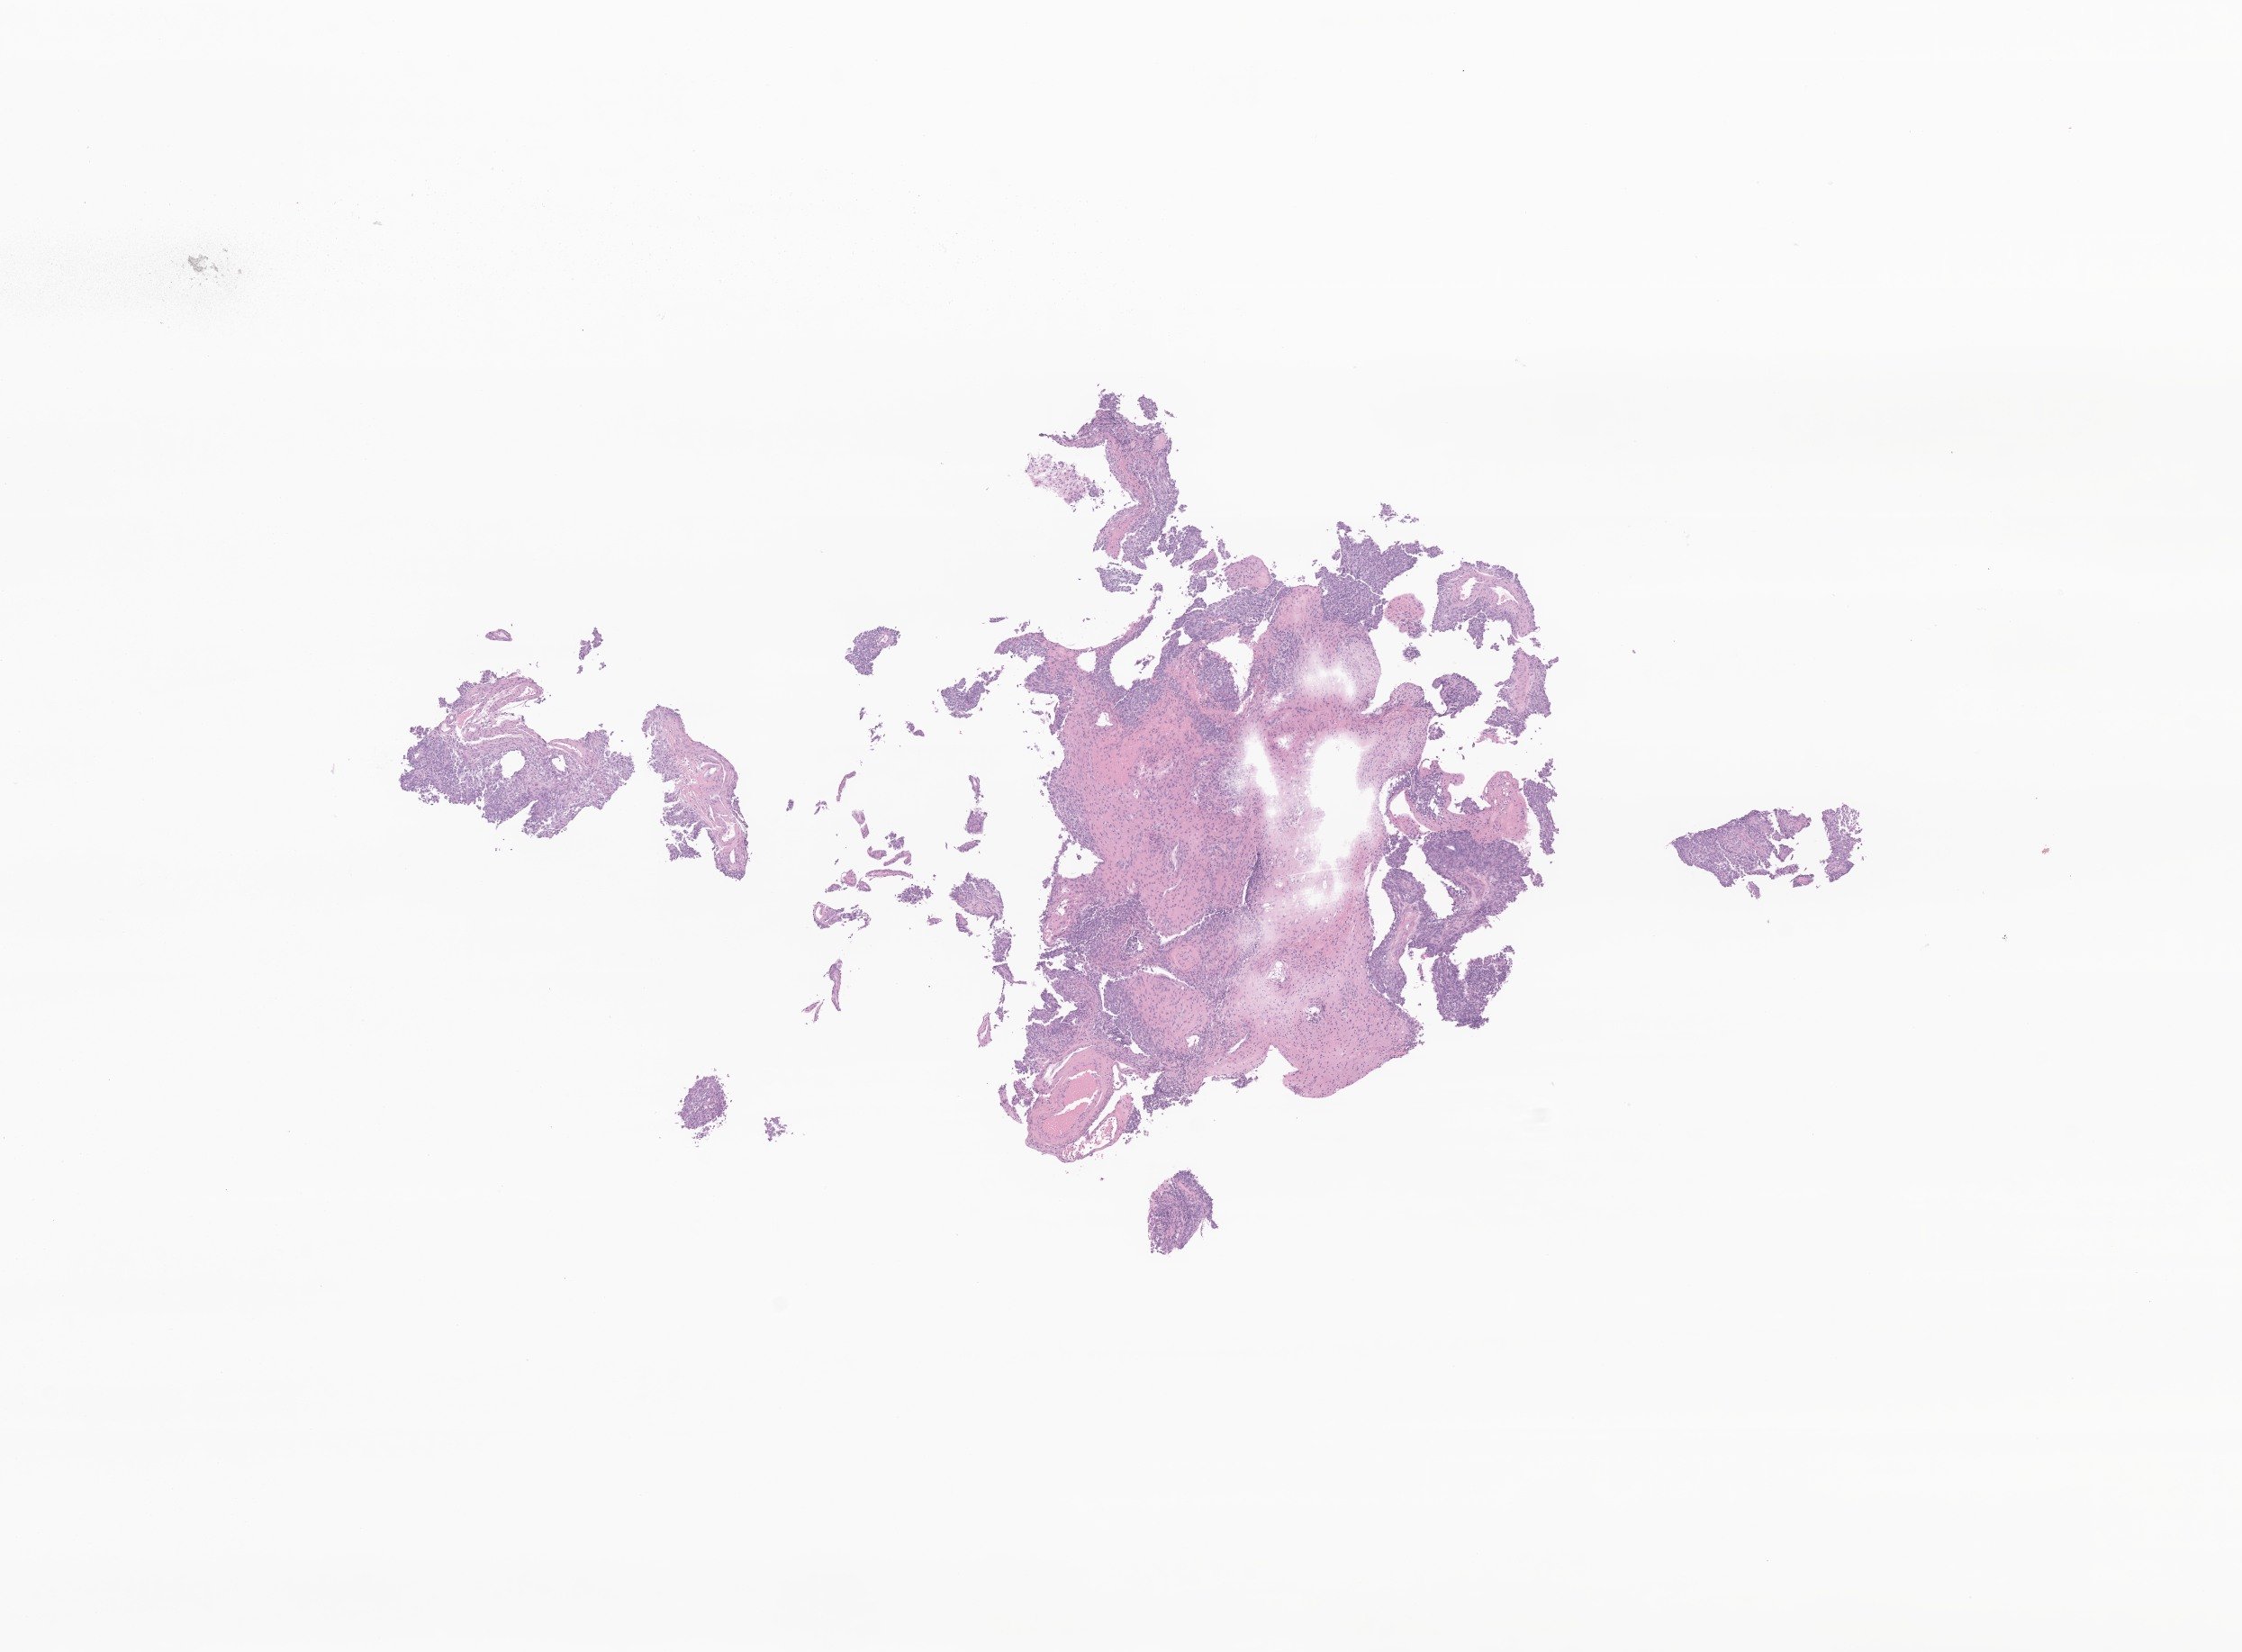
H&E whole-slide image of tumor tissue from the brain — low-resolution overview of the scanned area, about 10.5 x 7.7 mm, FFPE section. Patient female; age 126 days.
Diagnosis (ICD-O-3 morphology term): Atypical teratoid/rhabdoid tumor.